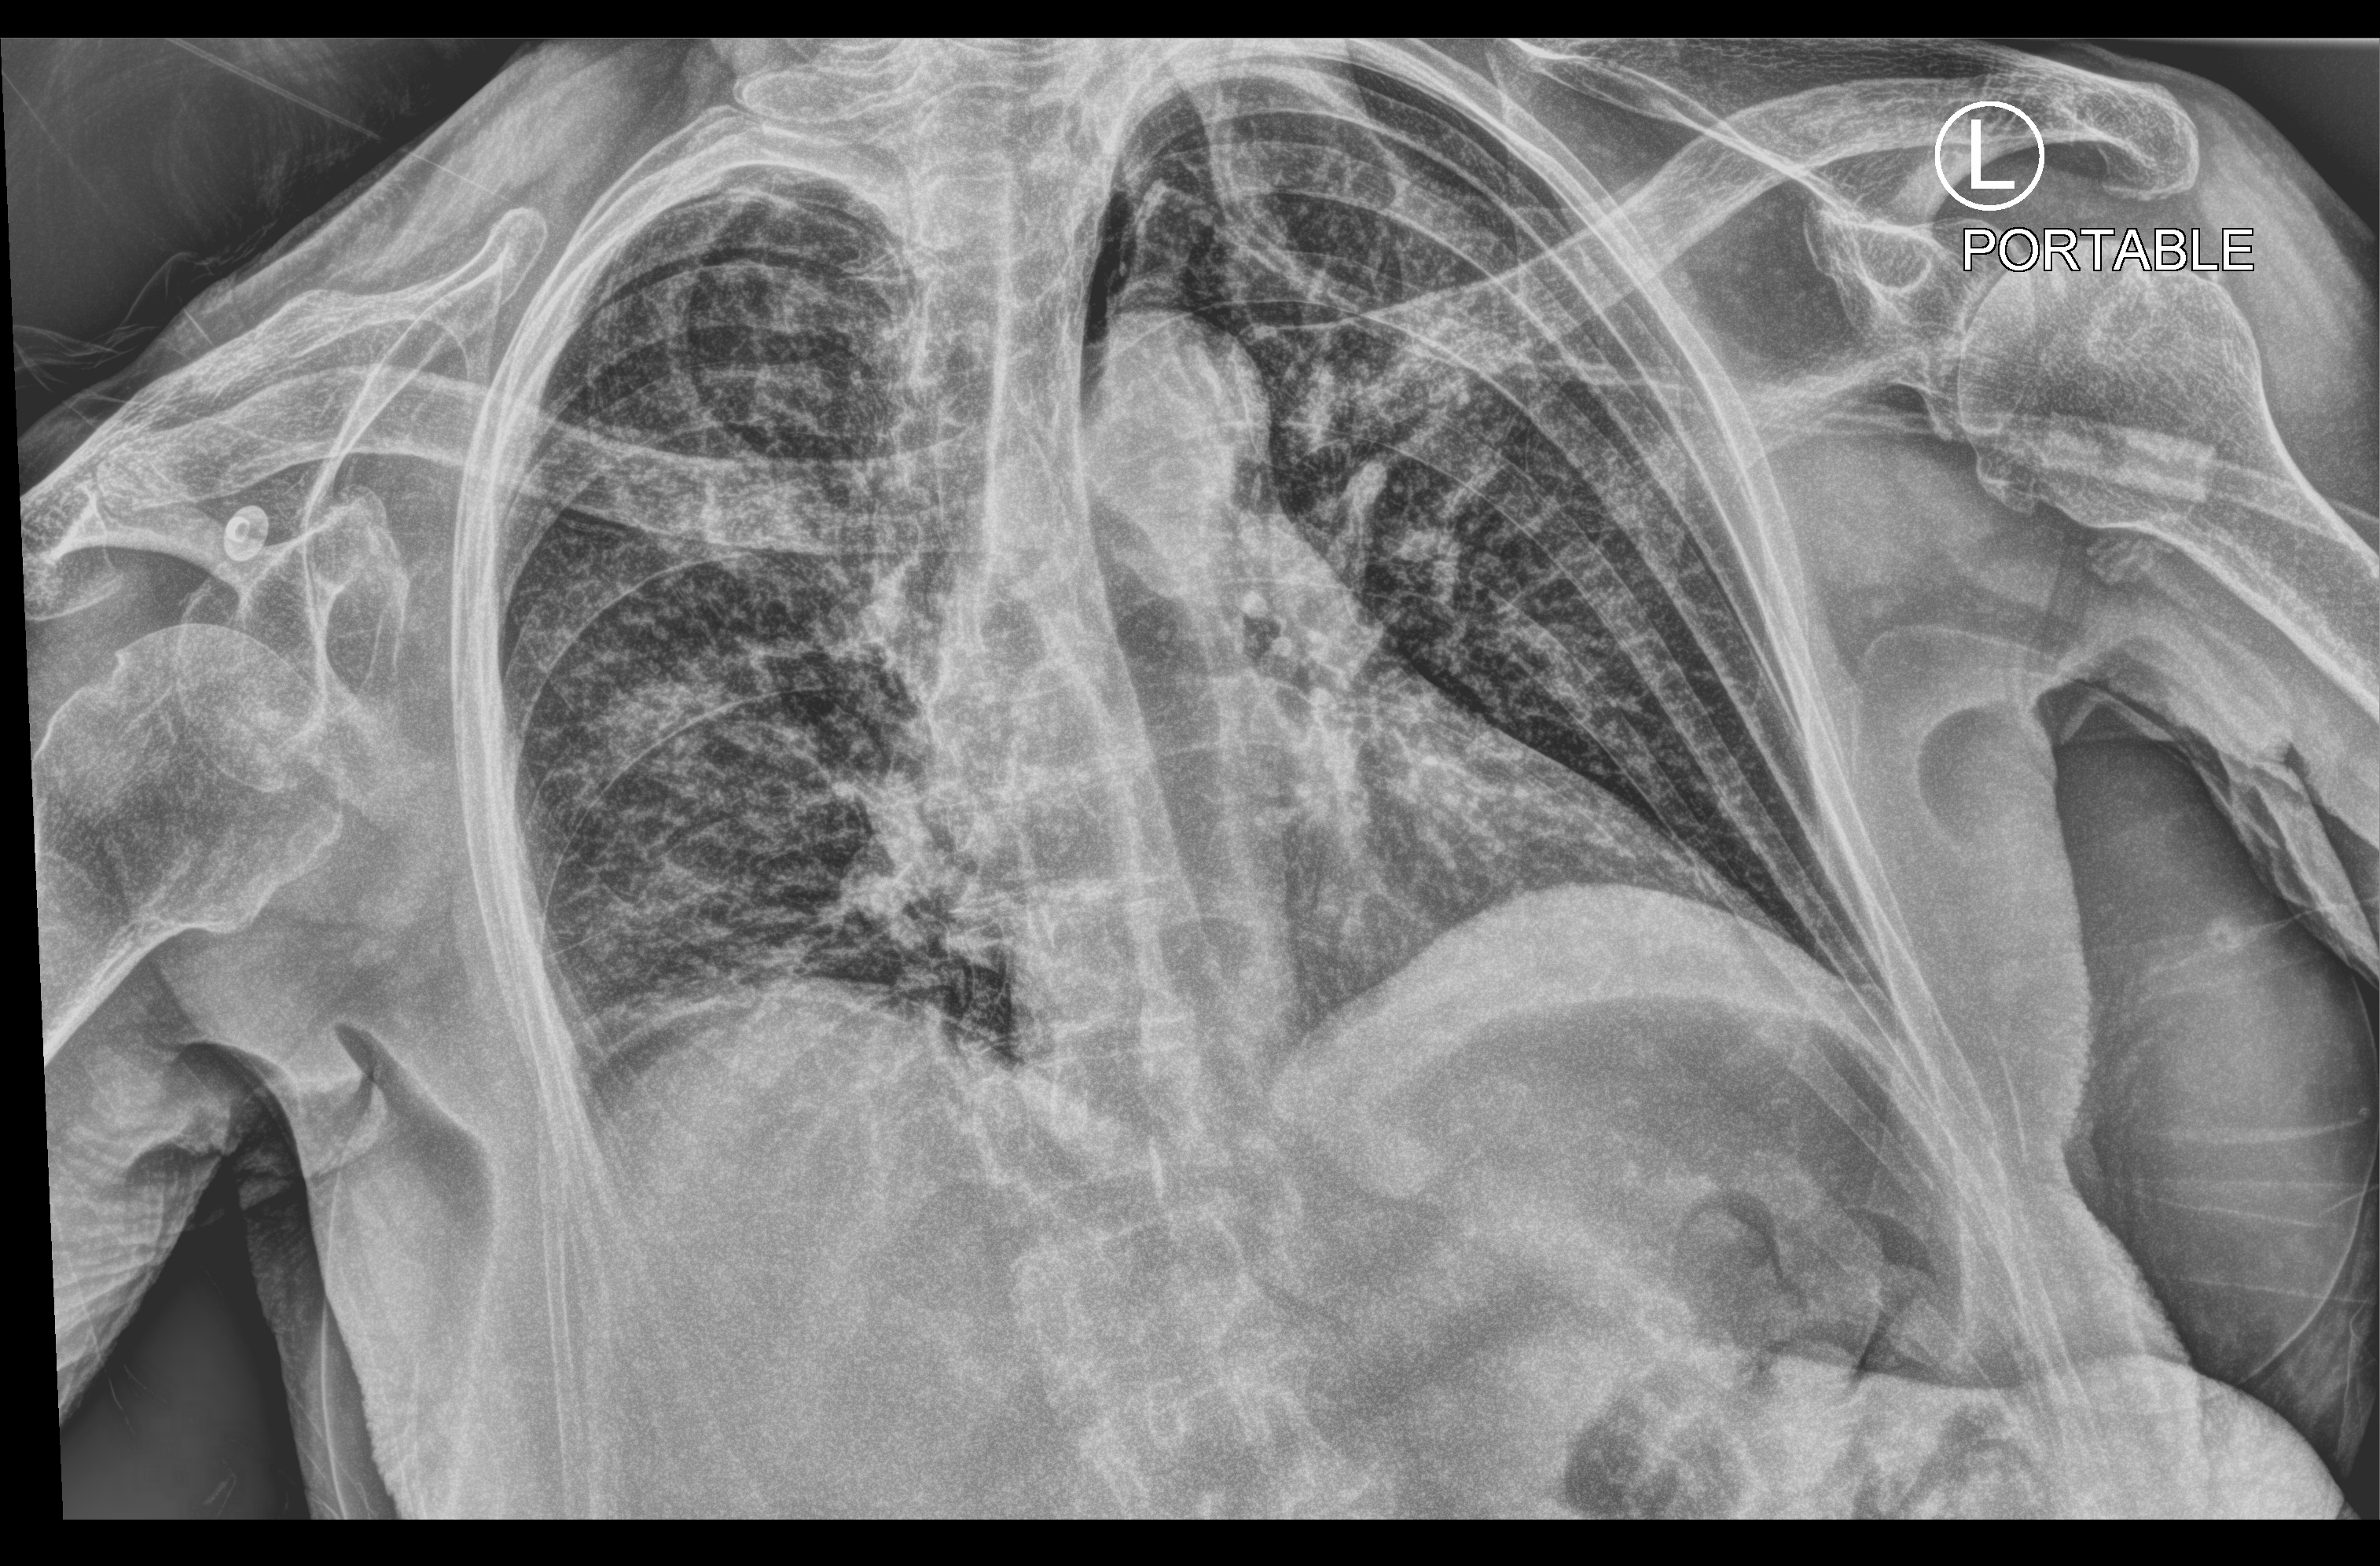
Portable chest radiograph, anteroposterior (AP) projection. Patient hospitalised with COVID-19; female, aged 60–74 years.
From the hospital-stay record, not from the radiograph (when in the stay this image was taken is not recorded):
- admitted to intensive care during this hospital stay: no
- mechanically ventilated during this hospital stay: no
- length of hospital stay: 13 days